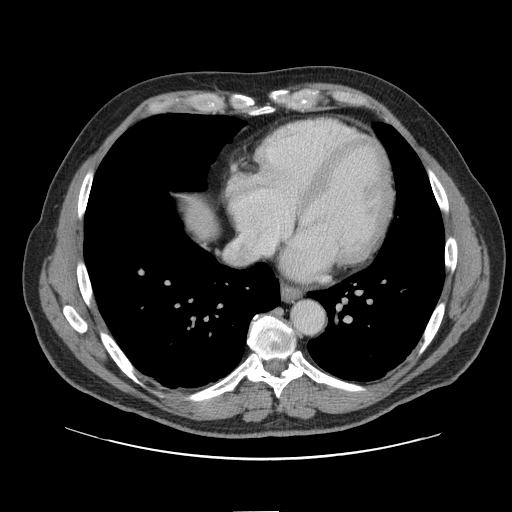
Contrast-enhanced abdominal CT, one axial slice; slice 145 of 161 in the series (ordered by position); intravenous contrast given; soft-tissue window (W 400 / L 40 HU); 2.5 mm slice thickness; 512 × 512 image matrix, field of view 412 × 412 mm. Male patient, age 66 years. Case-level facts recorded for this patient, not image findings: diagnosis: colorectal cancer liver metastases, imaged before liver resection; multiple liver metastases: no; largest metastasis: 3.5 cm; disease in both lobes: no.
Structures marked on this image (expert manual segmentation):
- liver: bounding box [x1, y1, x2, y2] px = [189, 207, 212, 235]
- planned liver remnant (the part of the liver to remain after resection): [189, 206, 212, 235]